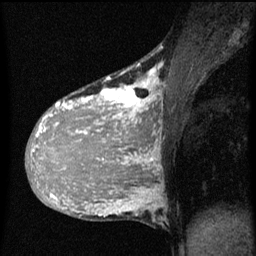
Breast MRI (dynamic contrast-enhanced), one sagittal slice; slice 28 of 60 in the series (ordered by position); dynamic contrast-enhanced series, image 2 of 3 at this slice position (ordered by acquisition); 1.5 T; TE 4.2 ms, TR 8 ms; 2 mm slice thickness; 256 × 256 image matrix. Patient: female, 36 years.
Annotated regions visible in this slice (semi-automatically segmented with operator editing):
- analysis volume of interest (the breast-tissue region the enhancement analysis was run in; not a lesion): bounding box <32,68,167,161> (left, top, right, bottom; pixels)
- tumour enhancement mask (voxels above the 70 % enhancement threshold inside the analysis volume of interest): <32,70,161,161>